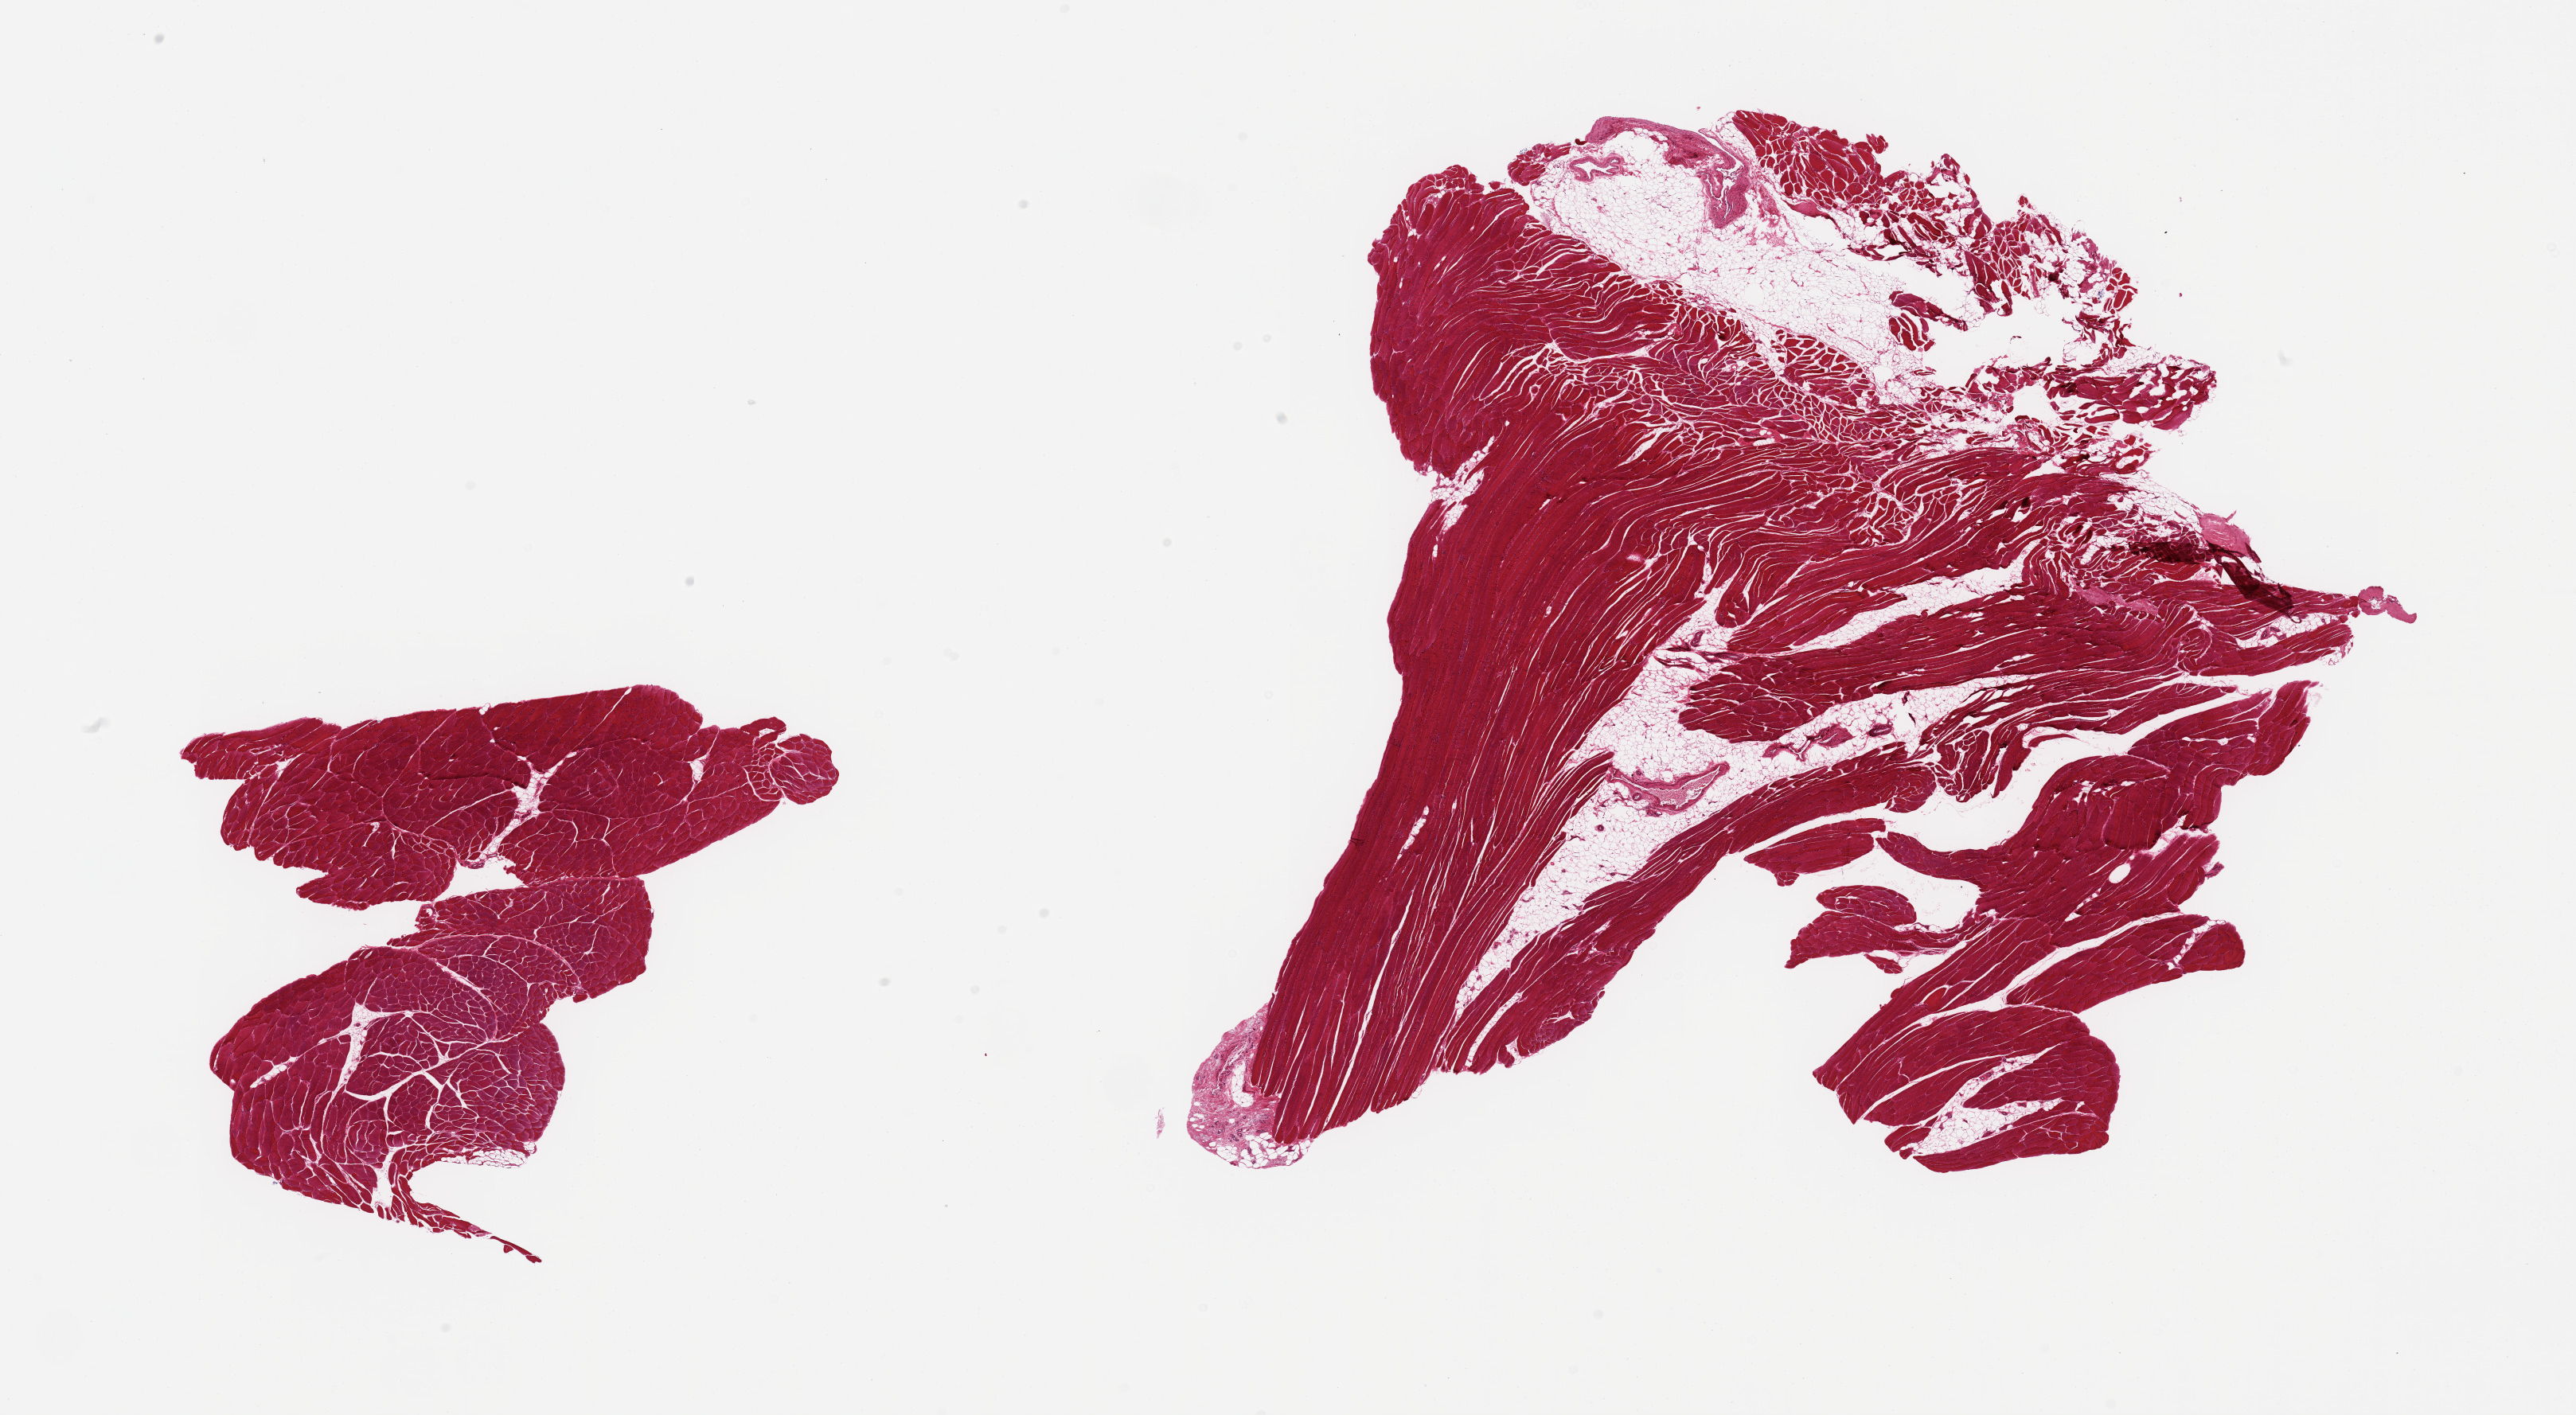
Whole-slide image, H&E stain — whole scanned area (about 25.6 x 14.1 mm) shown as a low-resolution overview; PAXgene-fixed, paraffin-embedded tissue; target tissue: skeletal muscle; donor tissue sample. Donor sex: male.
- pathologist's review note for this sample: 2 pieces, ~15-20% interstitial fat/vascular elements